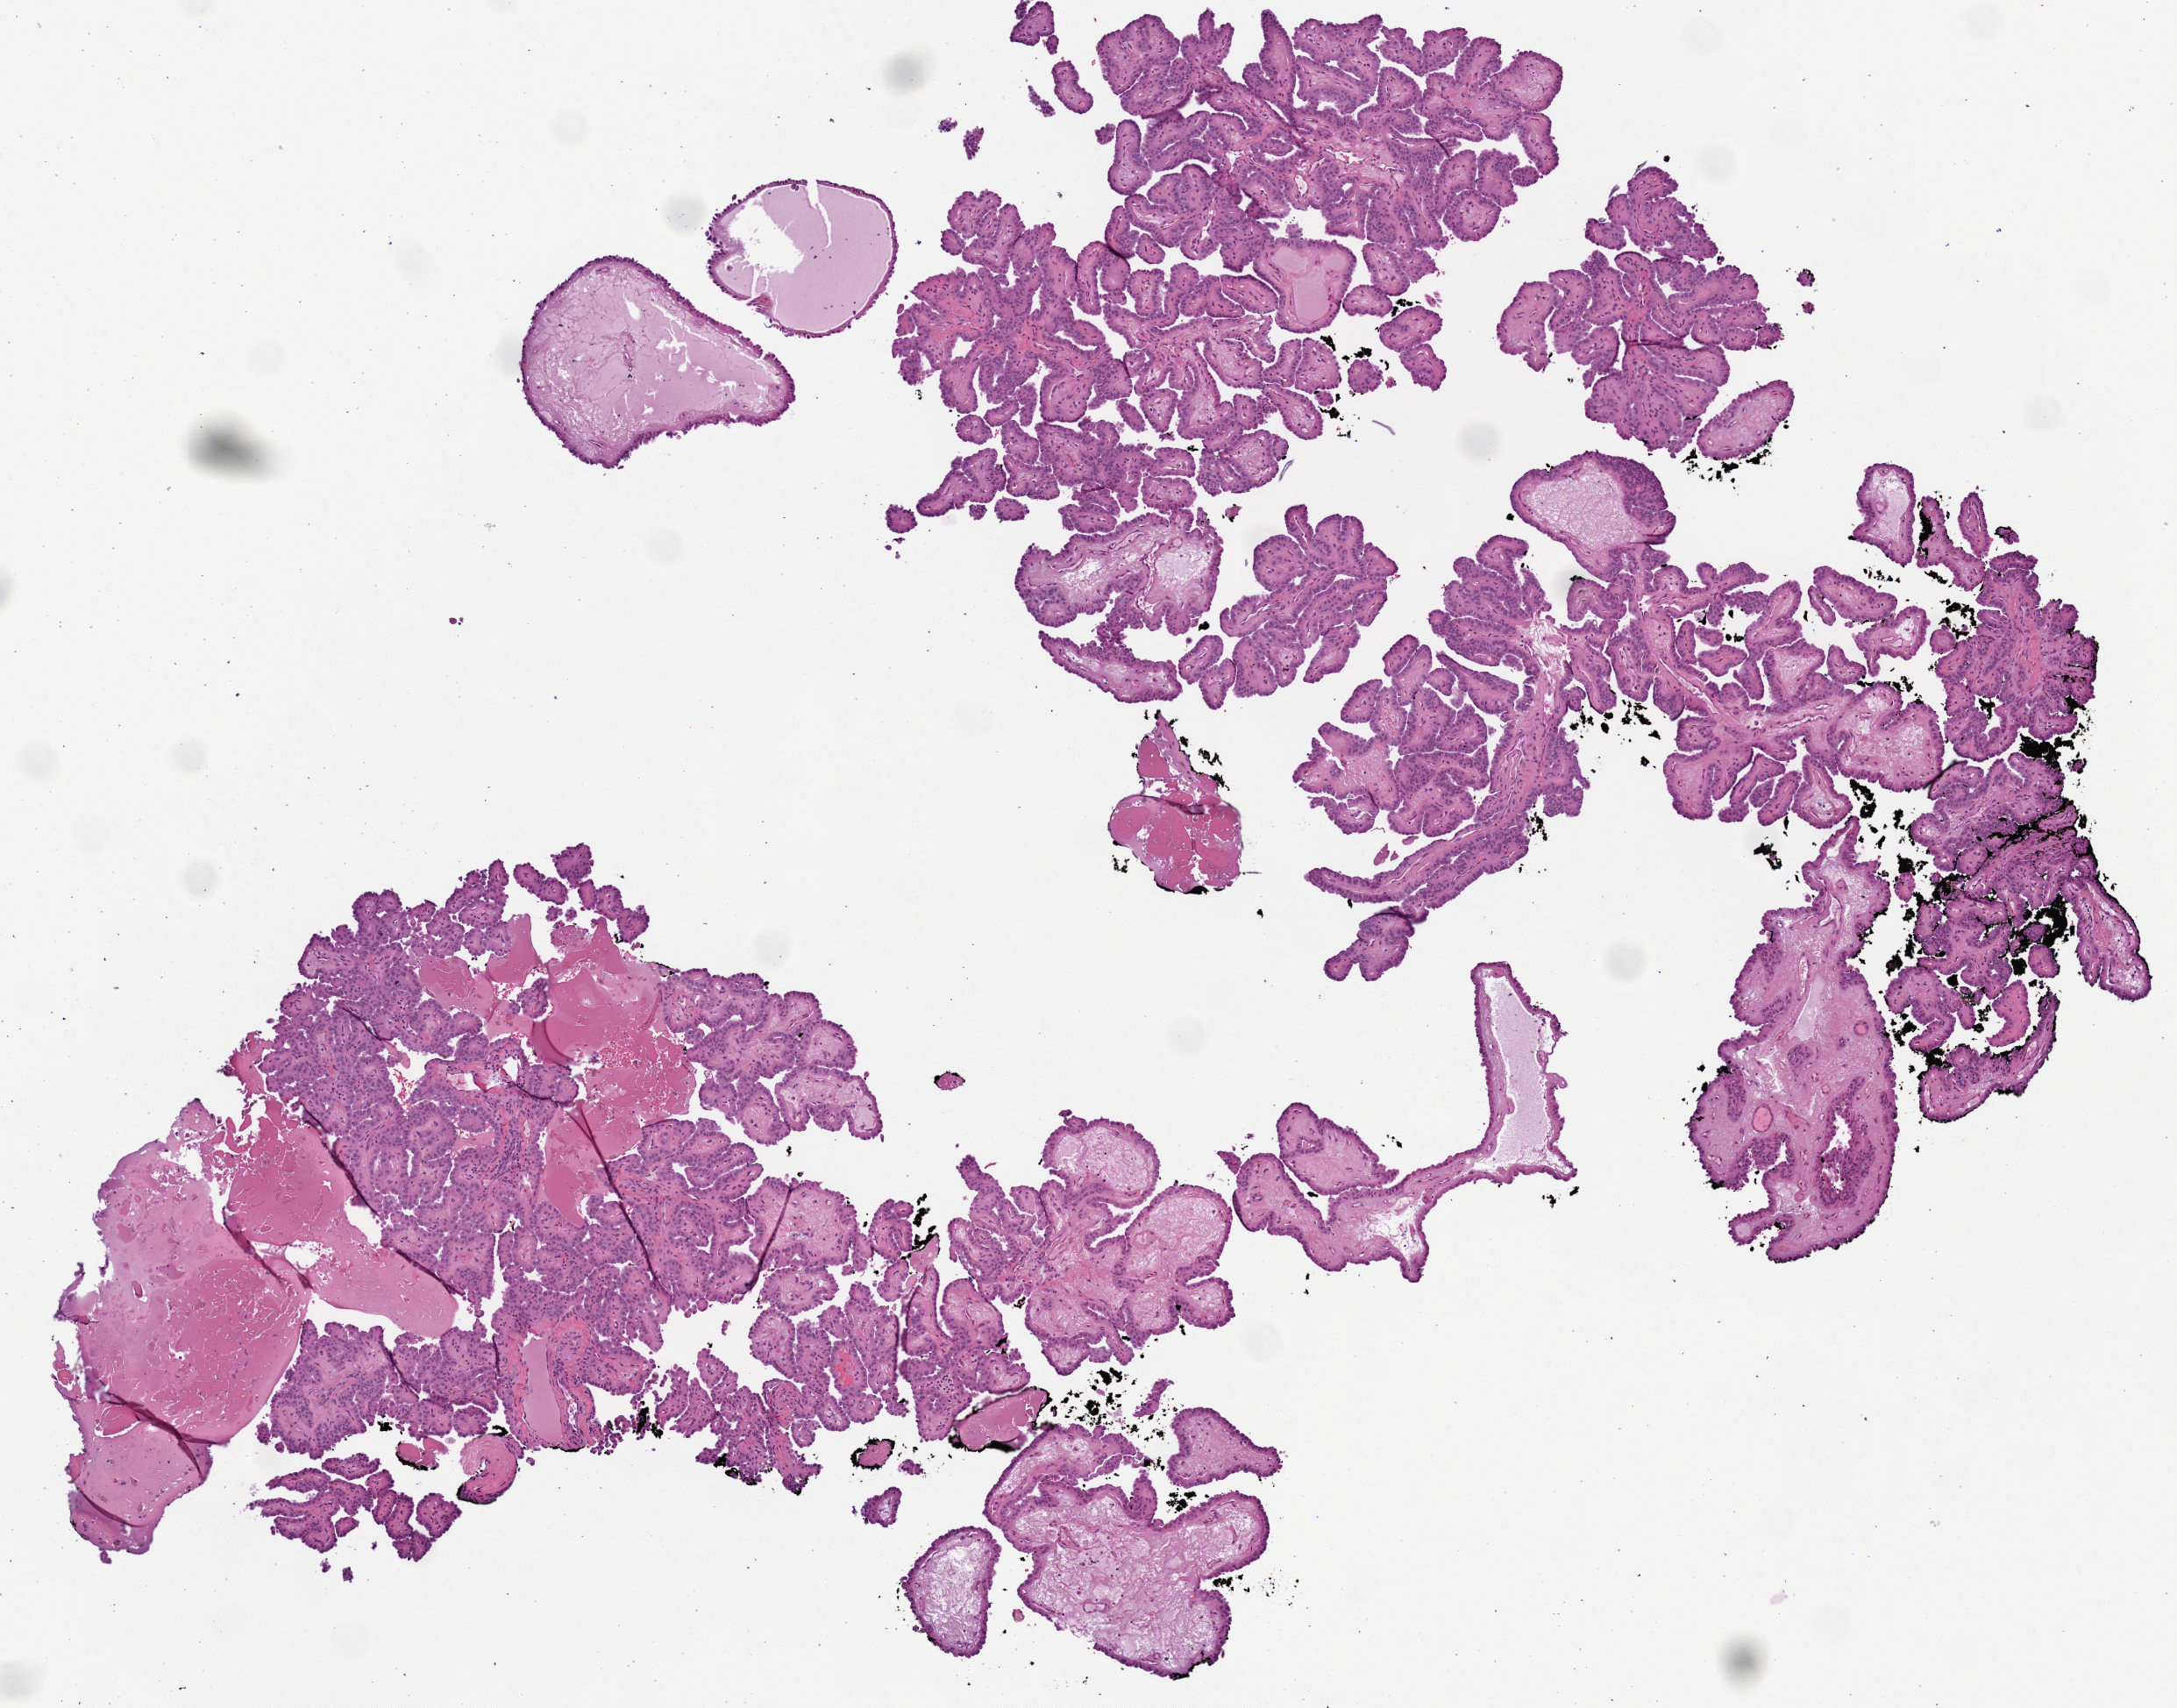
H&E-stained whole-slide image — low-resolution overview of the scanned area, about 5.0 x 3.9 mm (from a 40x scan); FFPE section; primary tumour sample from the thyroid. Female patient; age at initial diagnosis 21 years.
Pathologic diagnosis: Papillary adenocarcinoma, NOS (thyroid gland). AJCC pathologic stage: I (7th edition). TNM: T2 NX MX. Laterality: left.